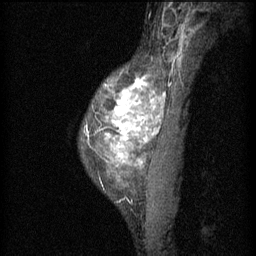
Breast MRI (dynamic contrast-enhanced), one sagittal slice. Position 43 of 60 along the scan axis. 3 images stored at this slice position (order not interpretable as contrast timing). 1.5 T. TE 4.2 ms, TR 11 ms. 2 mm slice thickness. 256 × 256 image matrix, field of view 180 × 180 mm. Patient: female, 40 years.
Structures marked on this image (semi-automatic segmentation, software-assisted and operator-edited):
- analysis volume of interest (the breast-tissue region the enhancement analysis was run in; not a lesion): bounding box [x1, y1, x2, y2] px = [82, 68, 166, 203]
- tumour enhancement mask (voxels above the 70 % enhancement threshold inside the analysis volume of interest): [87, 78, 166, 167]